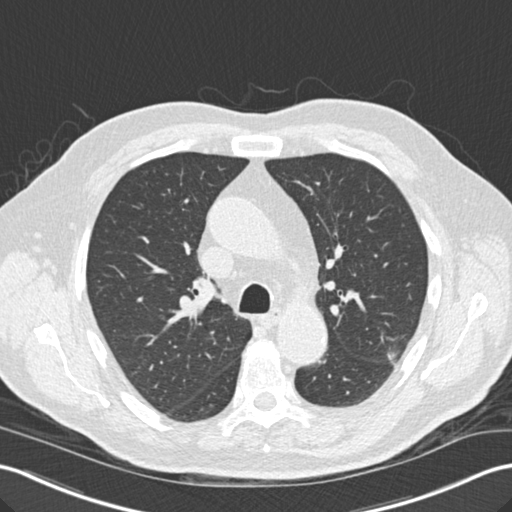
Low-dose screening chest CT, one axial slice; slice 101 of 157 in the series (ordered by position); lung window (W 1500 / L -600 HU); 2 mm slice thickness; 512 × 512 image matrix, field of view 354 × 354 mm.
Annotated regions visible in this slice (expert manual segmentation):
- lesion 1 (tumor, upper lobe of left lung): bounding box (x1, y1, x2, y2) in pixels: (388, 354, 400, 367)